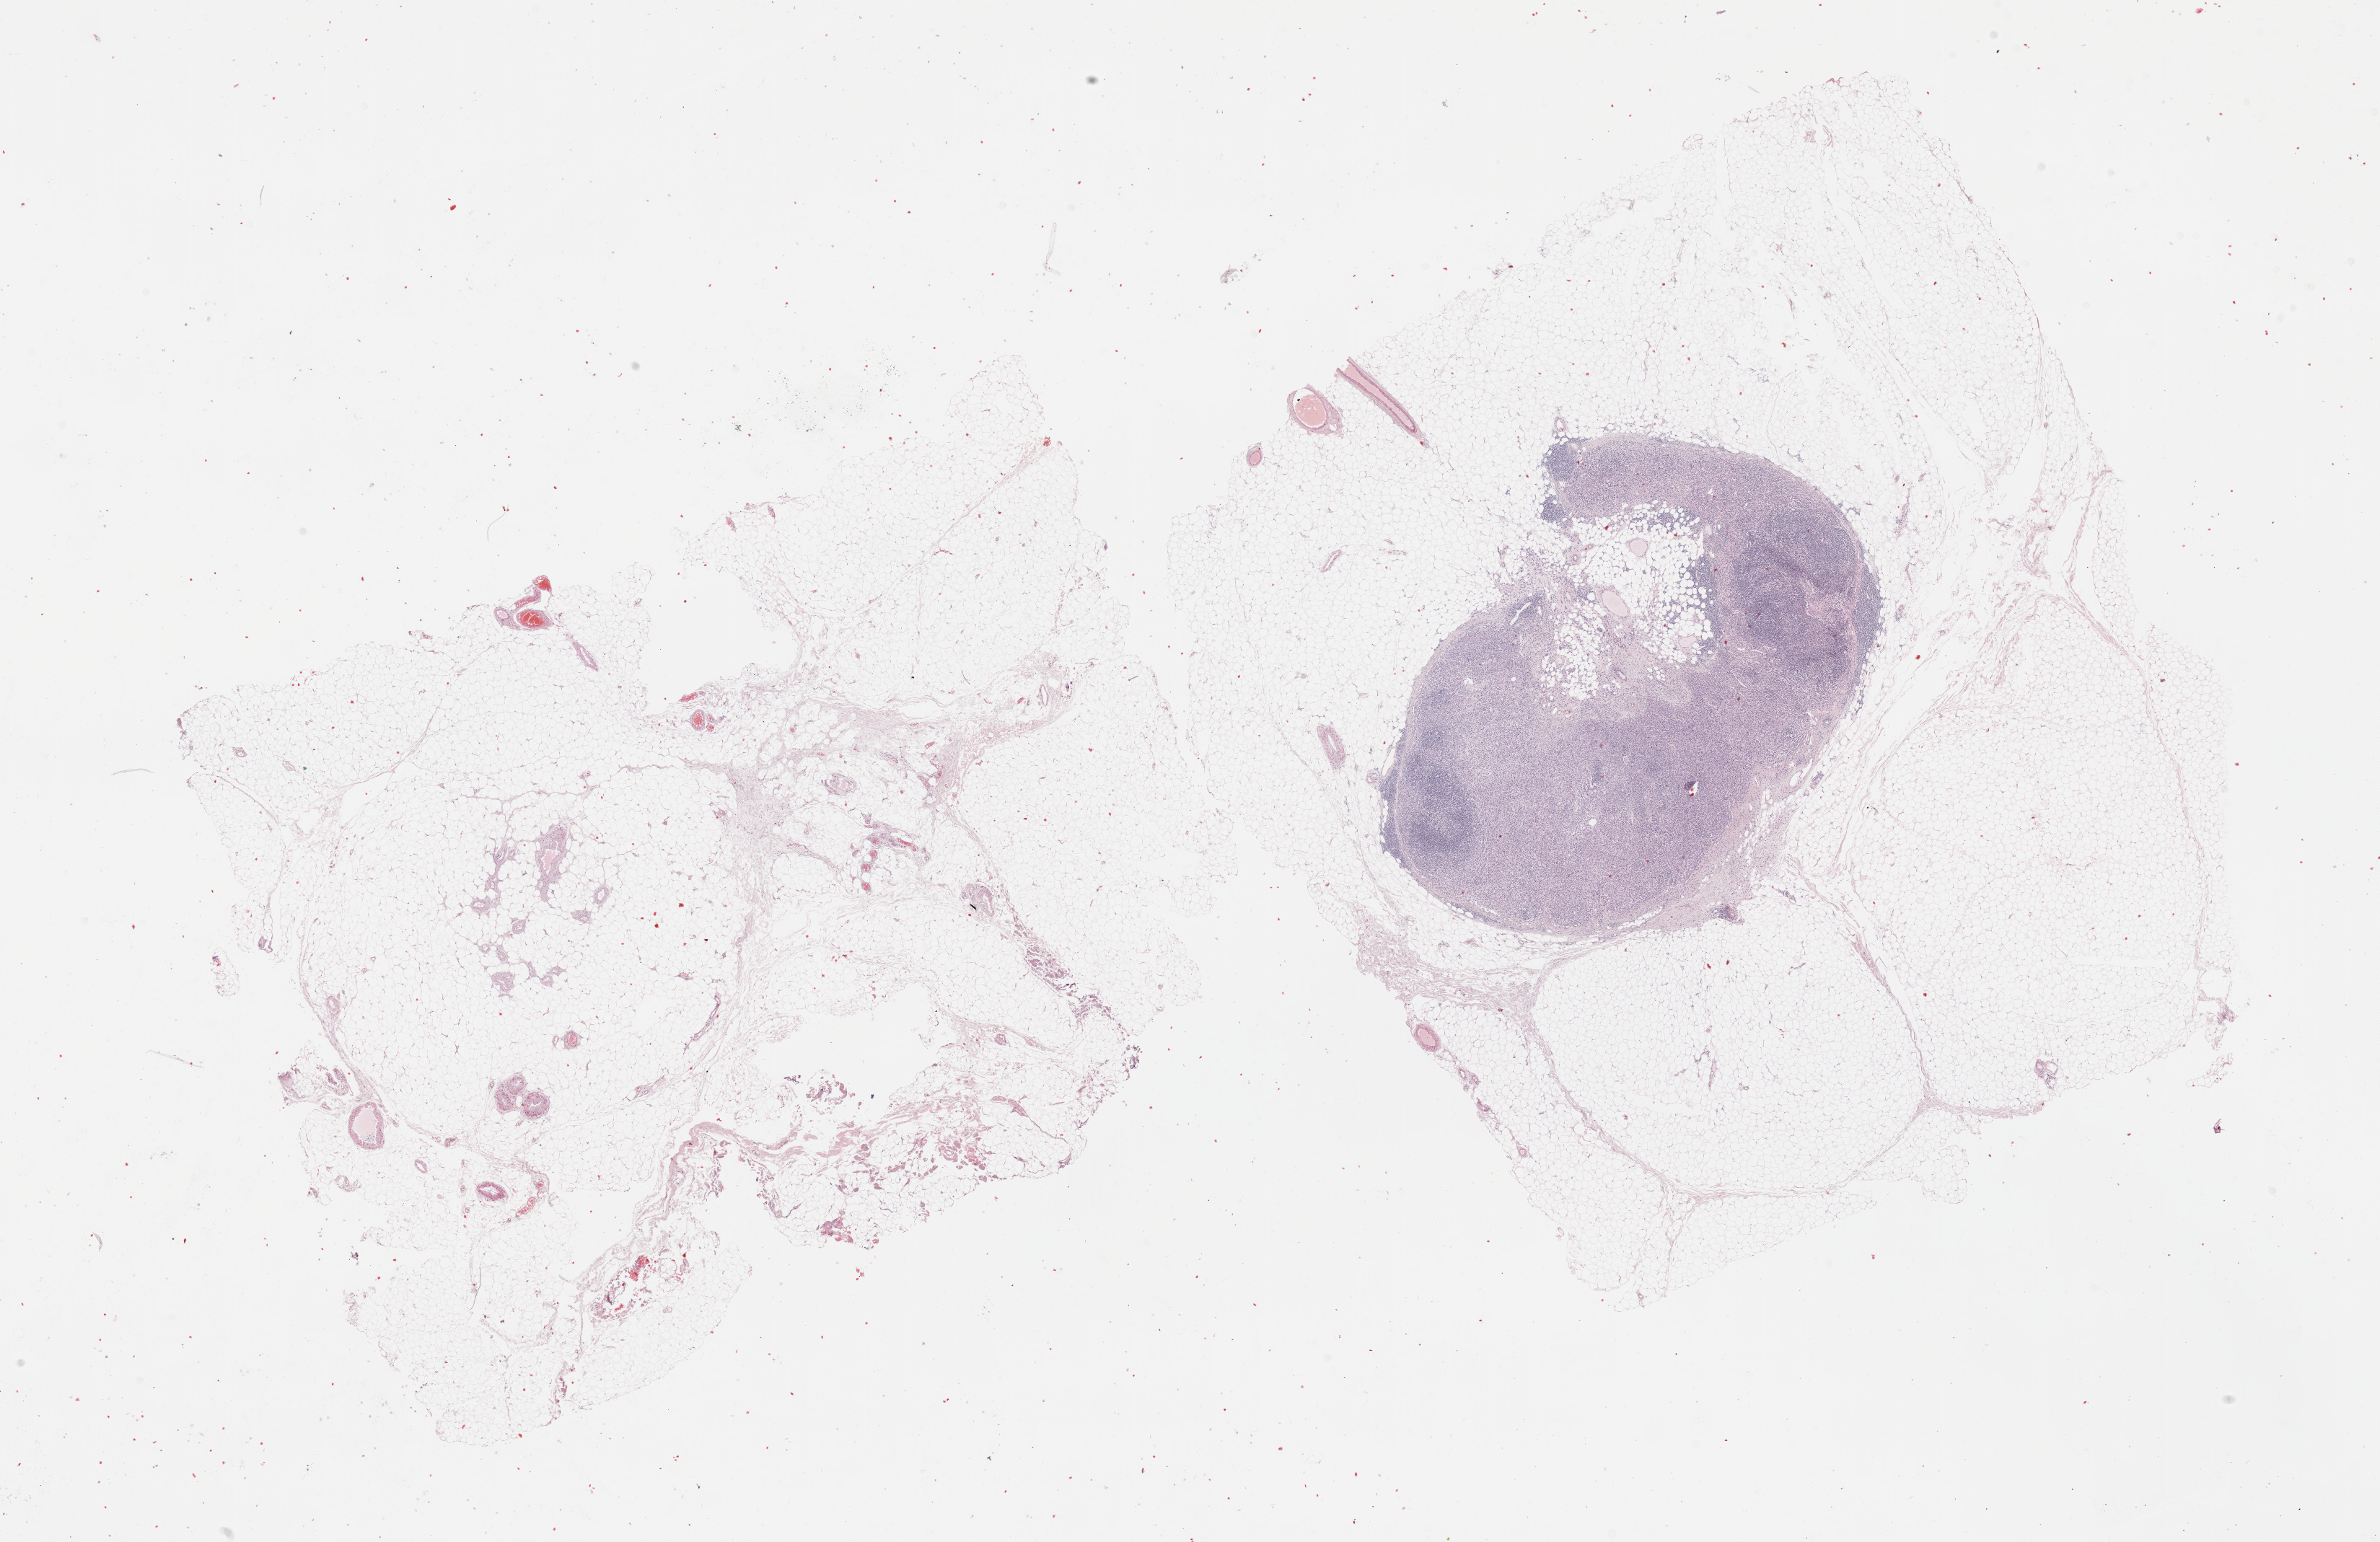
Digitized H&E tissue section (whole slide) — shown as a low-resolution overview of the whole scanned area (about 26.7 x 17.3 mm). Formalin-fixed paraffin-embedded (FFPE) diagnostic section. Primary tumour sample from the breast. Female, age 53 years at initial diagnosis.
TNM: T2 N3a M0. AJCC pathologic stage: IIIC. Lymph nodes positive (case pathology): 12 of 12 examined. Diagnosis: Lobular carcinoma, NOS.